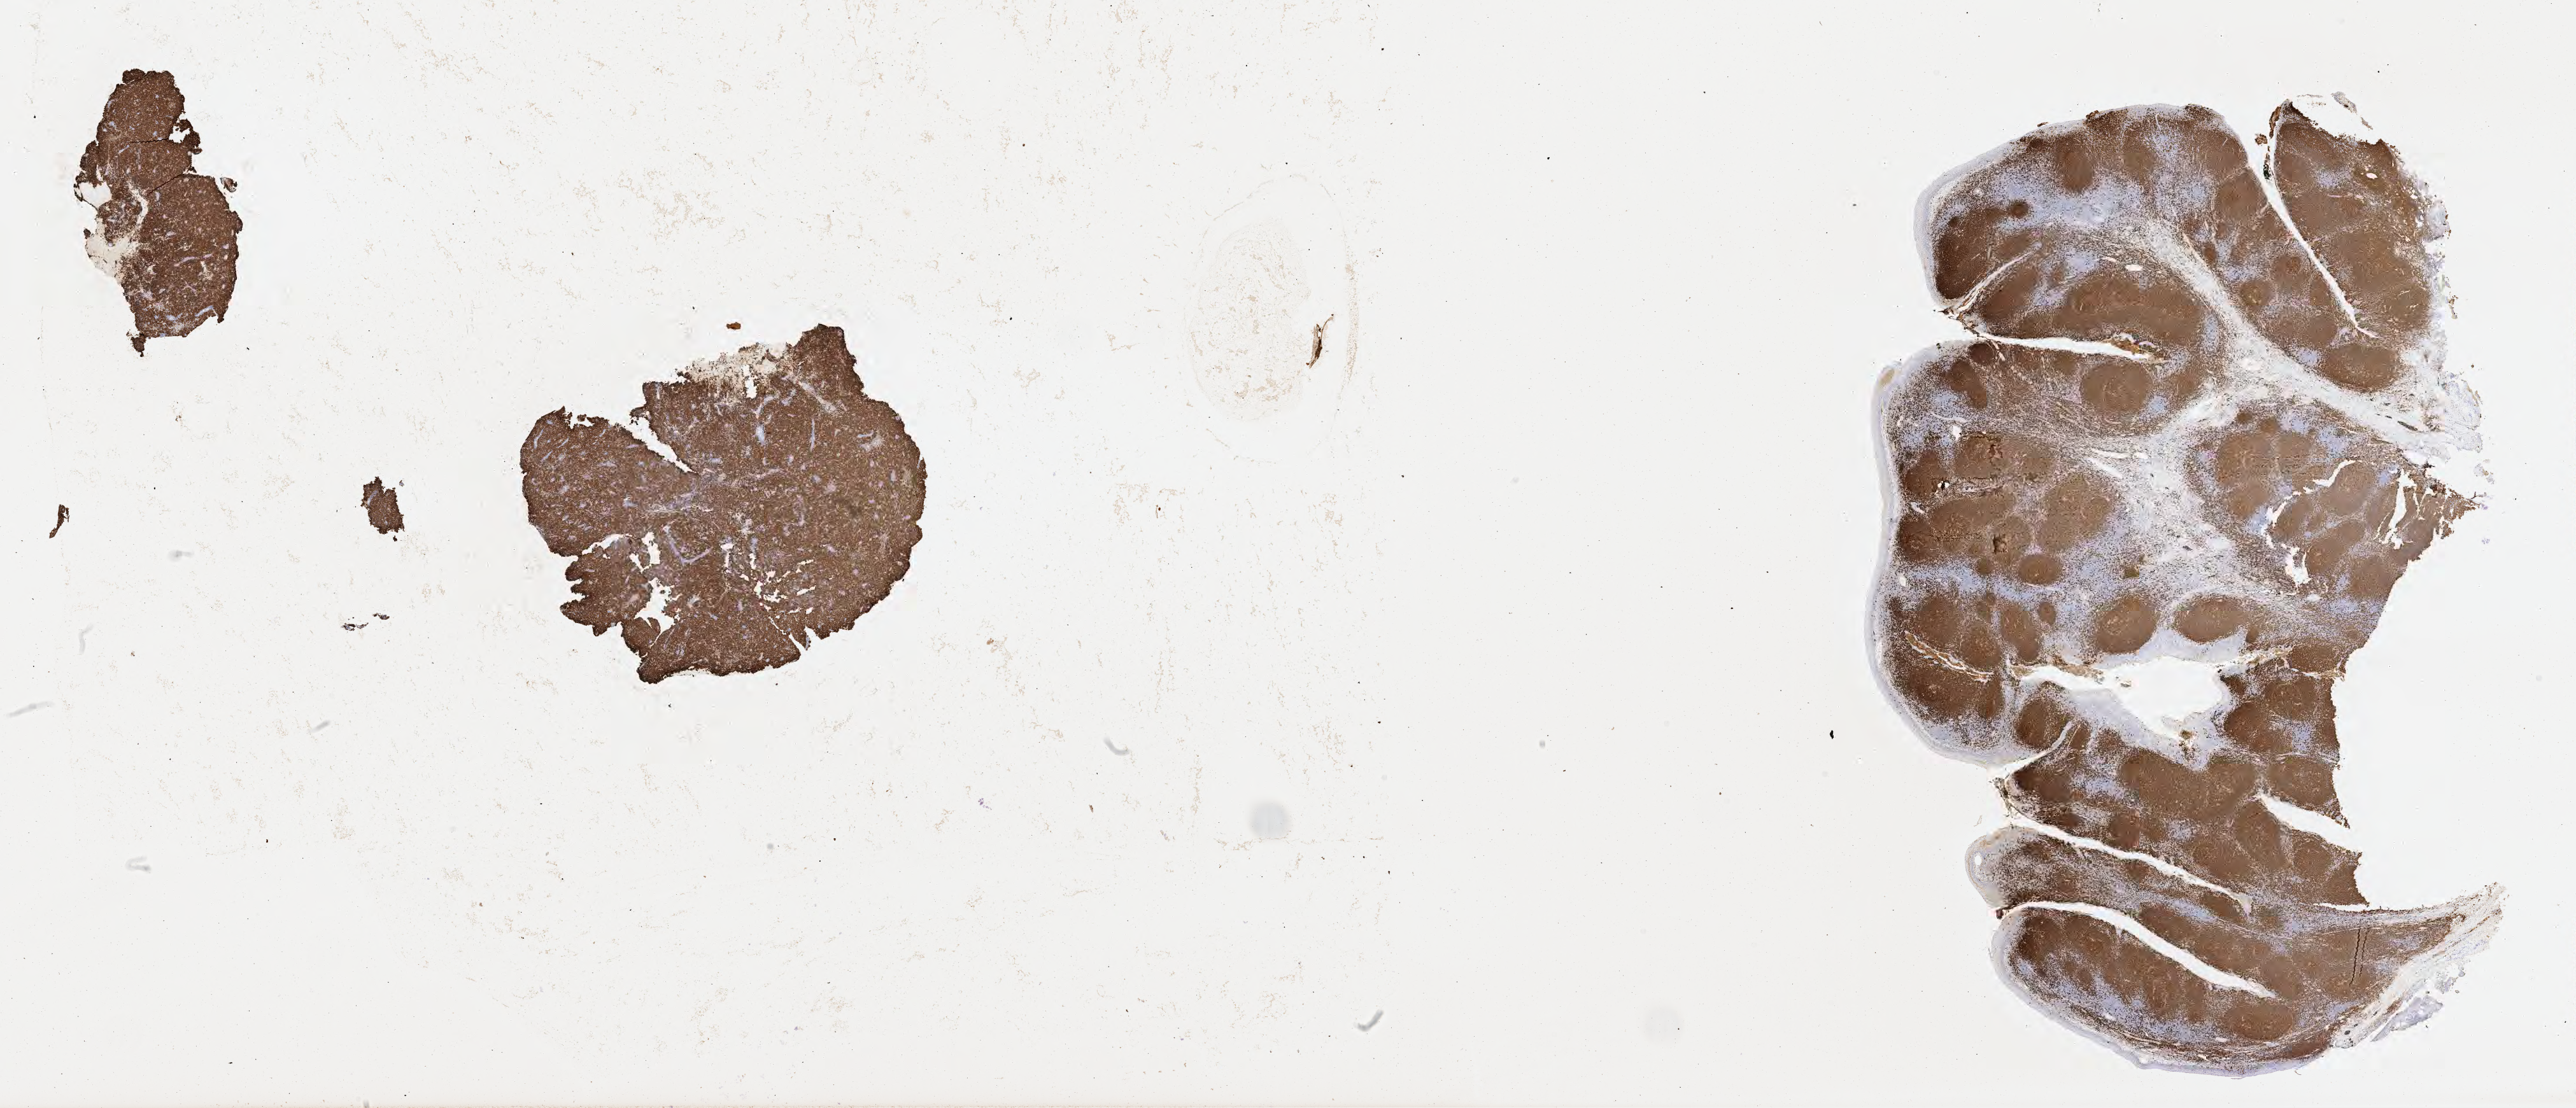
Immunohistochemistry (IHC) whole-slide image stained for CD20 — whole scanned area (about 32.7 x 14.1 mm) shown as a low-resolution overview; tumor tissue; anatomic site: lymph node. Patient female; age 51 years.
- histologic diagnosis: Diffuse large B-cell lymphoma, NOS